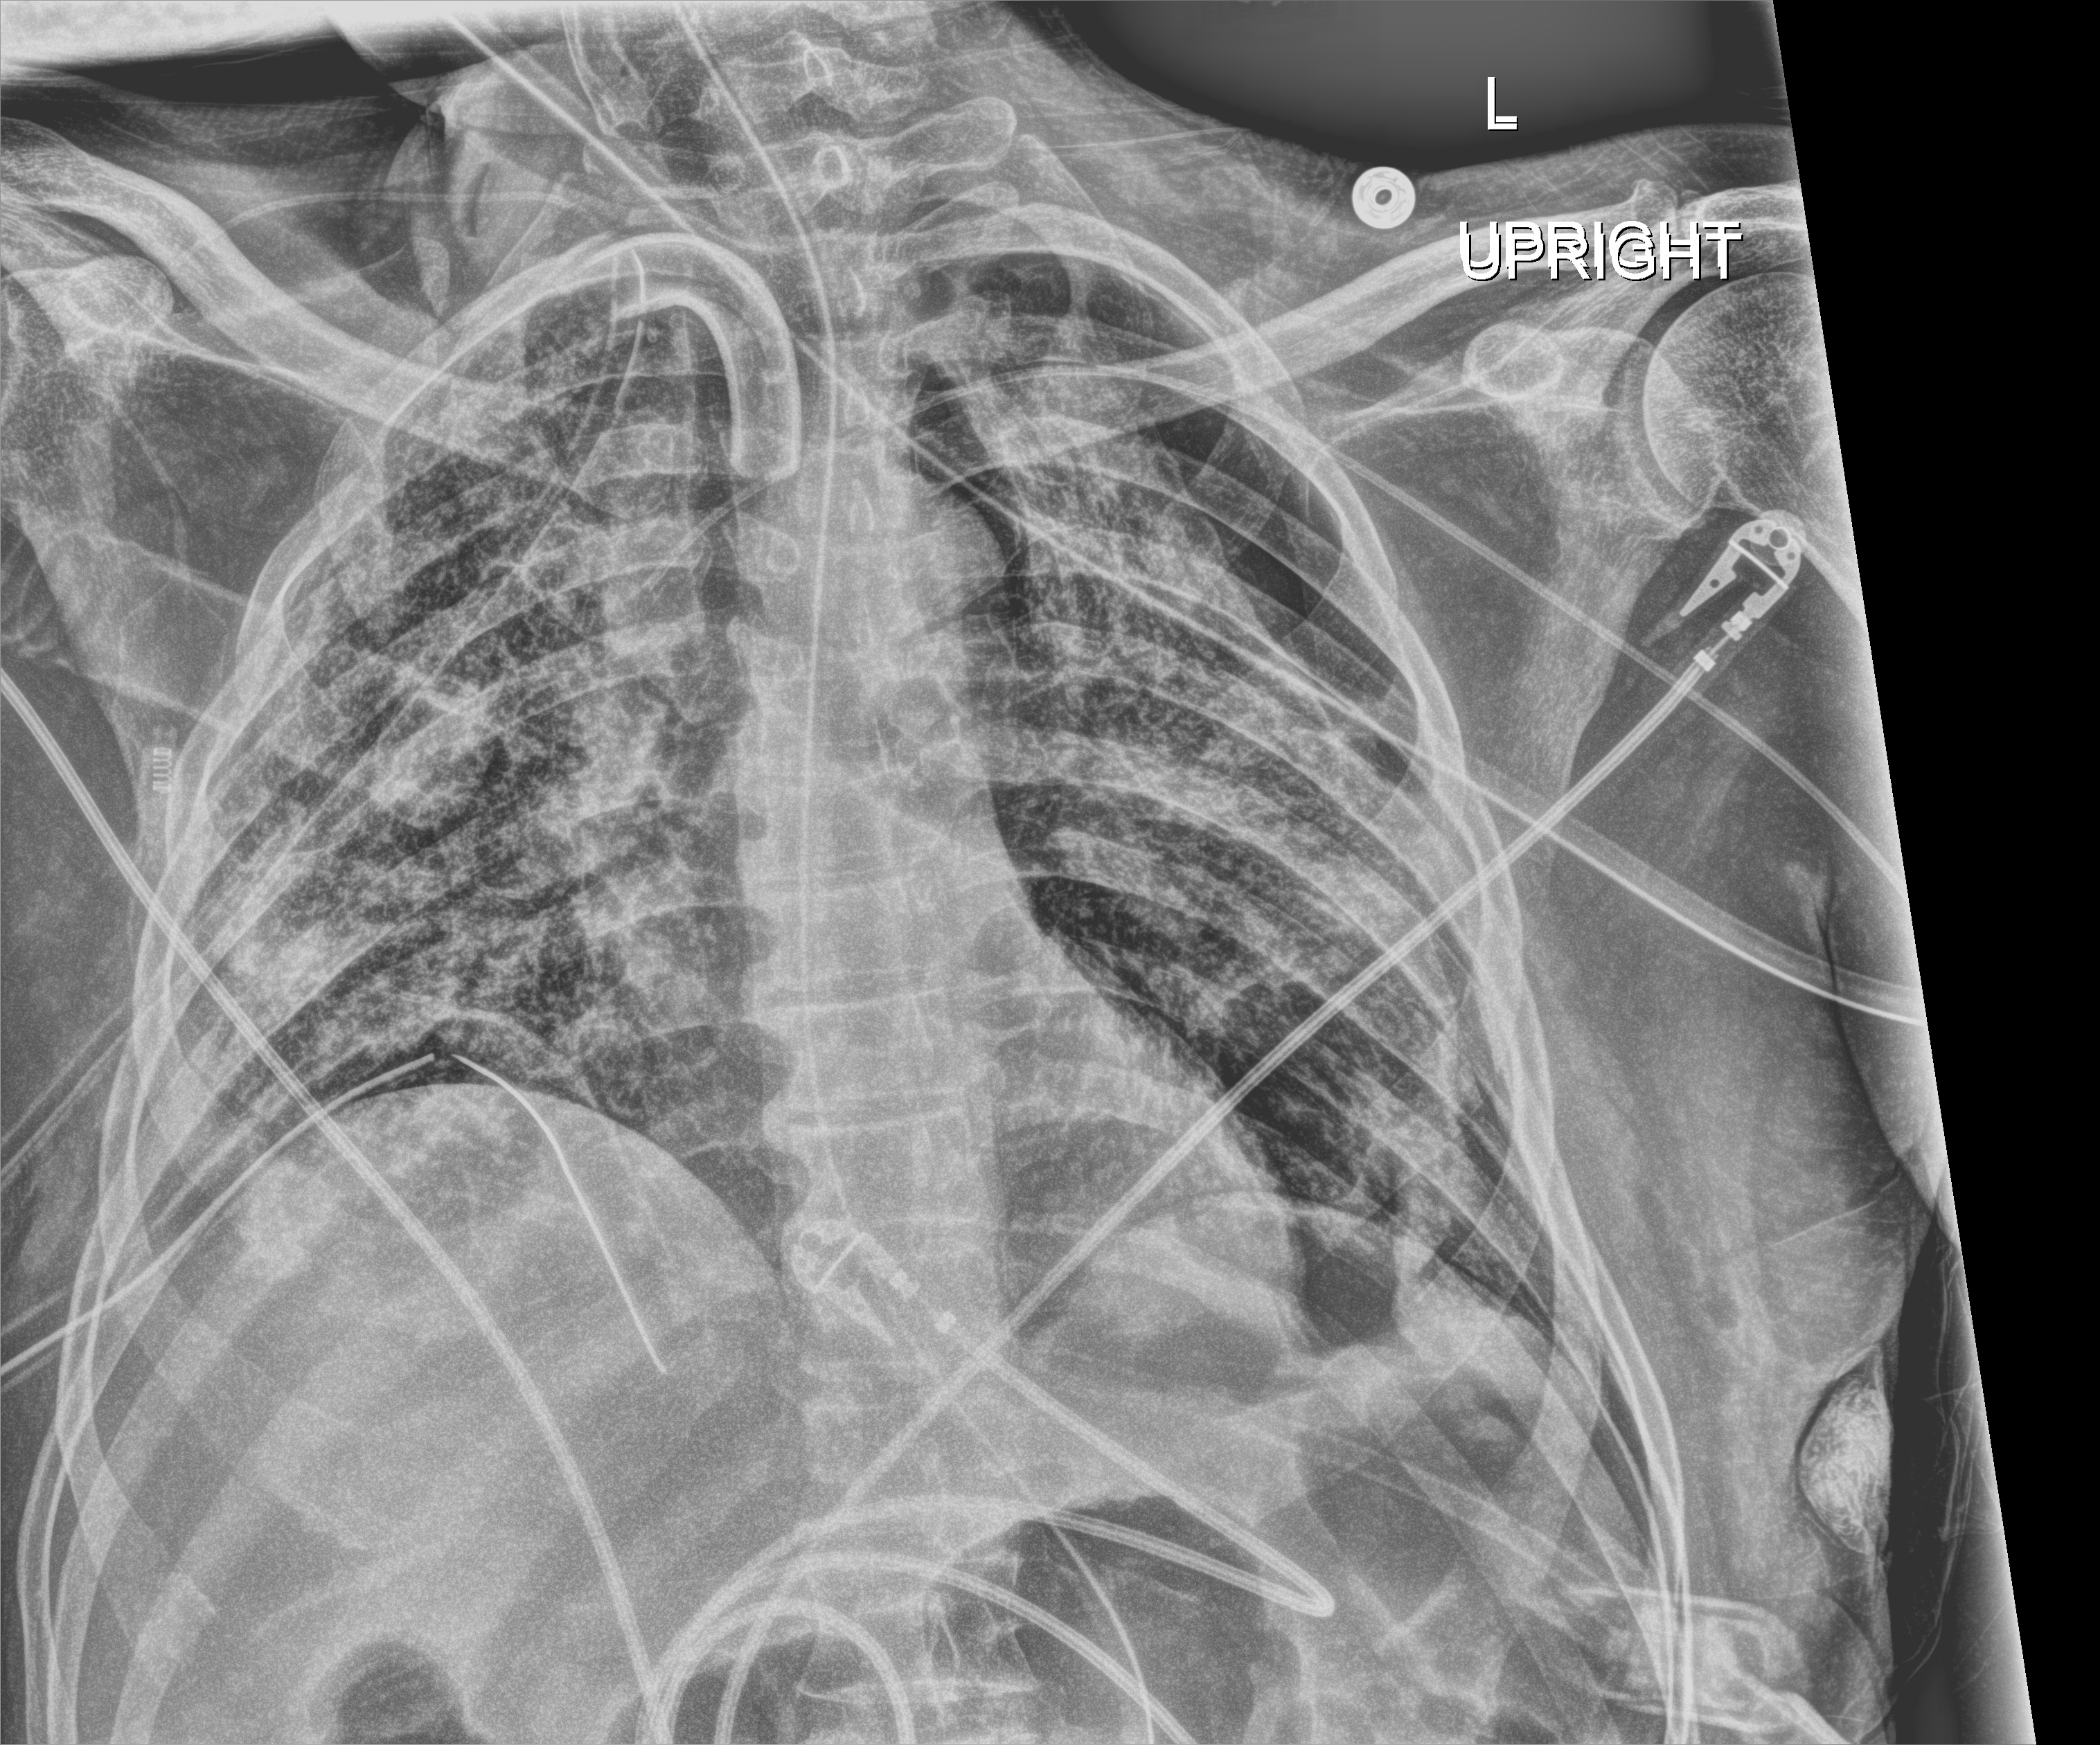
Bedside chest radiograph (digital radiography); anteroposterior (AP) projection. Patient hospitalised with COVID-19; male, aged 18–59 years.
Admission-level facts for this patient (not findings on this image; timing relative to this image not recorded): admitted to intensive care during this hospital stay: yes.